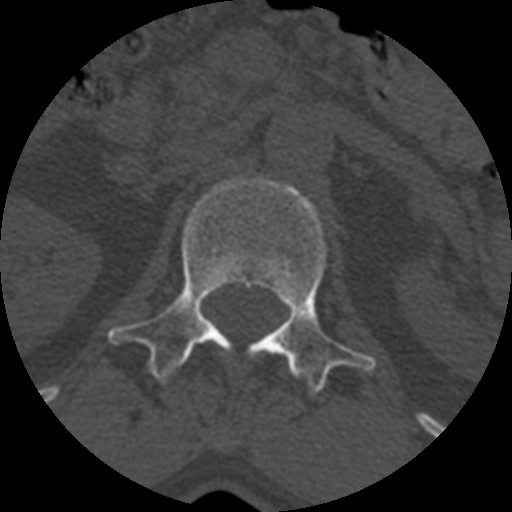
CT including the spine, one axial slice; reconstruction kernel STANDARD; 120 kVp; bone window (W 1800 / L 400 HU); 1.25 mm slice thickness; 512 × 512 image matrix, field of view 160 × 160 mm. Patient age 71 years. From the clinical record (not read from this slice): primary cancer: prostate.
Annotated regions visible in this slice (semi-automatically segmented with operator editing):
- L1 vertebra: bounding box <110,178,374,398> (left, top, right, bottom; pixels)